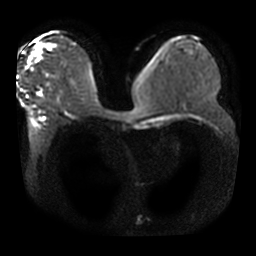
Breast MRI, one axial slice; position 17 of 42 along the scan axis; diffusion-weighted series; image 2 of 4 stored at this slice position (different b-values; order by instance number); 3 T; 256 × 256 image matrix. Female patient.
Outlined on this slice (outlined manually by an expert reader):
- tumour on diffusion-weighted imaging: bounding box <29,43,50,60> (left, top, right, bottom; pixels)